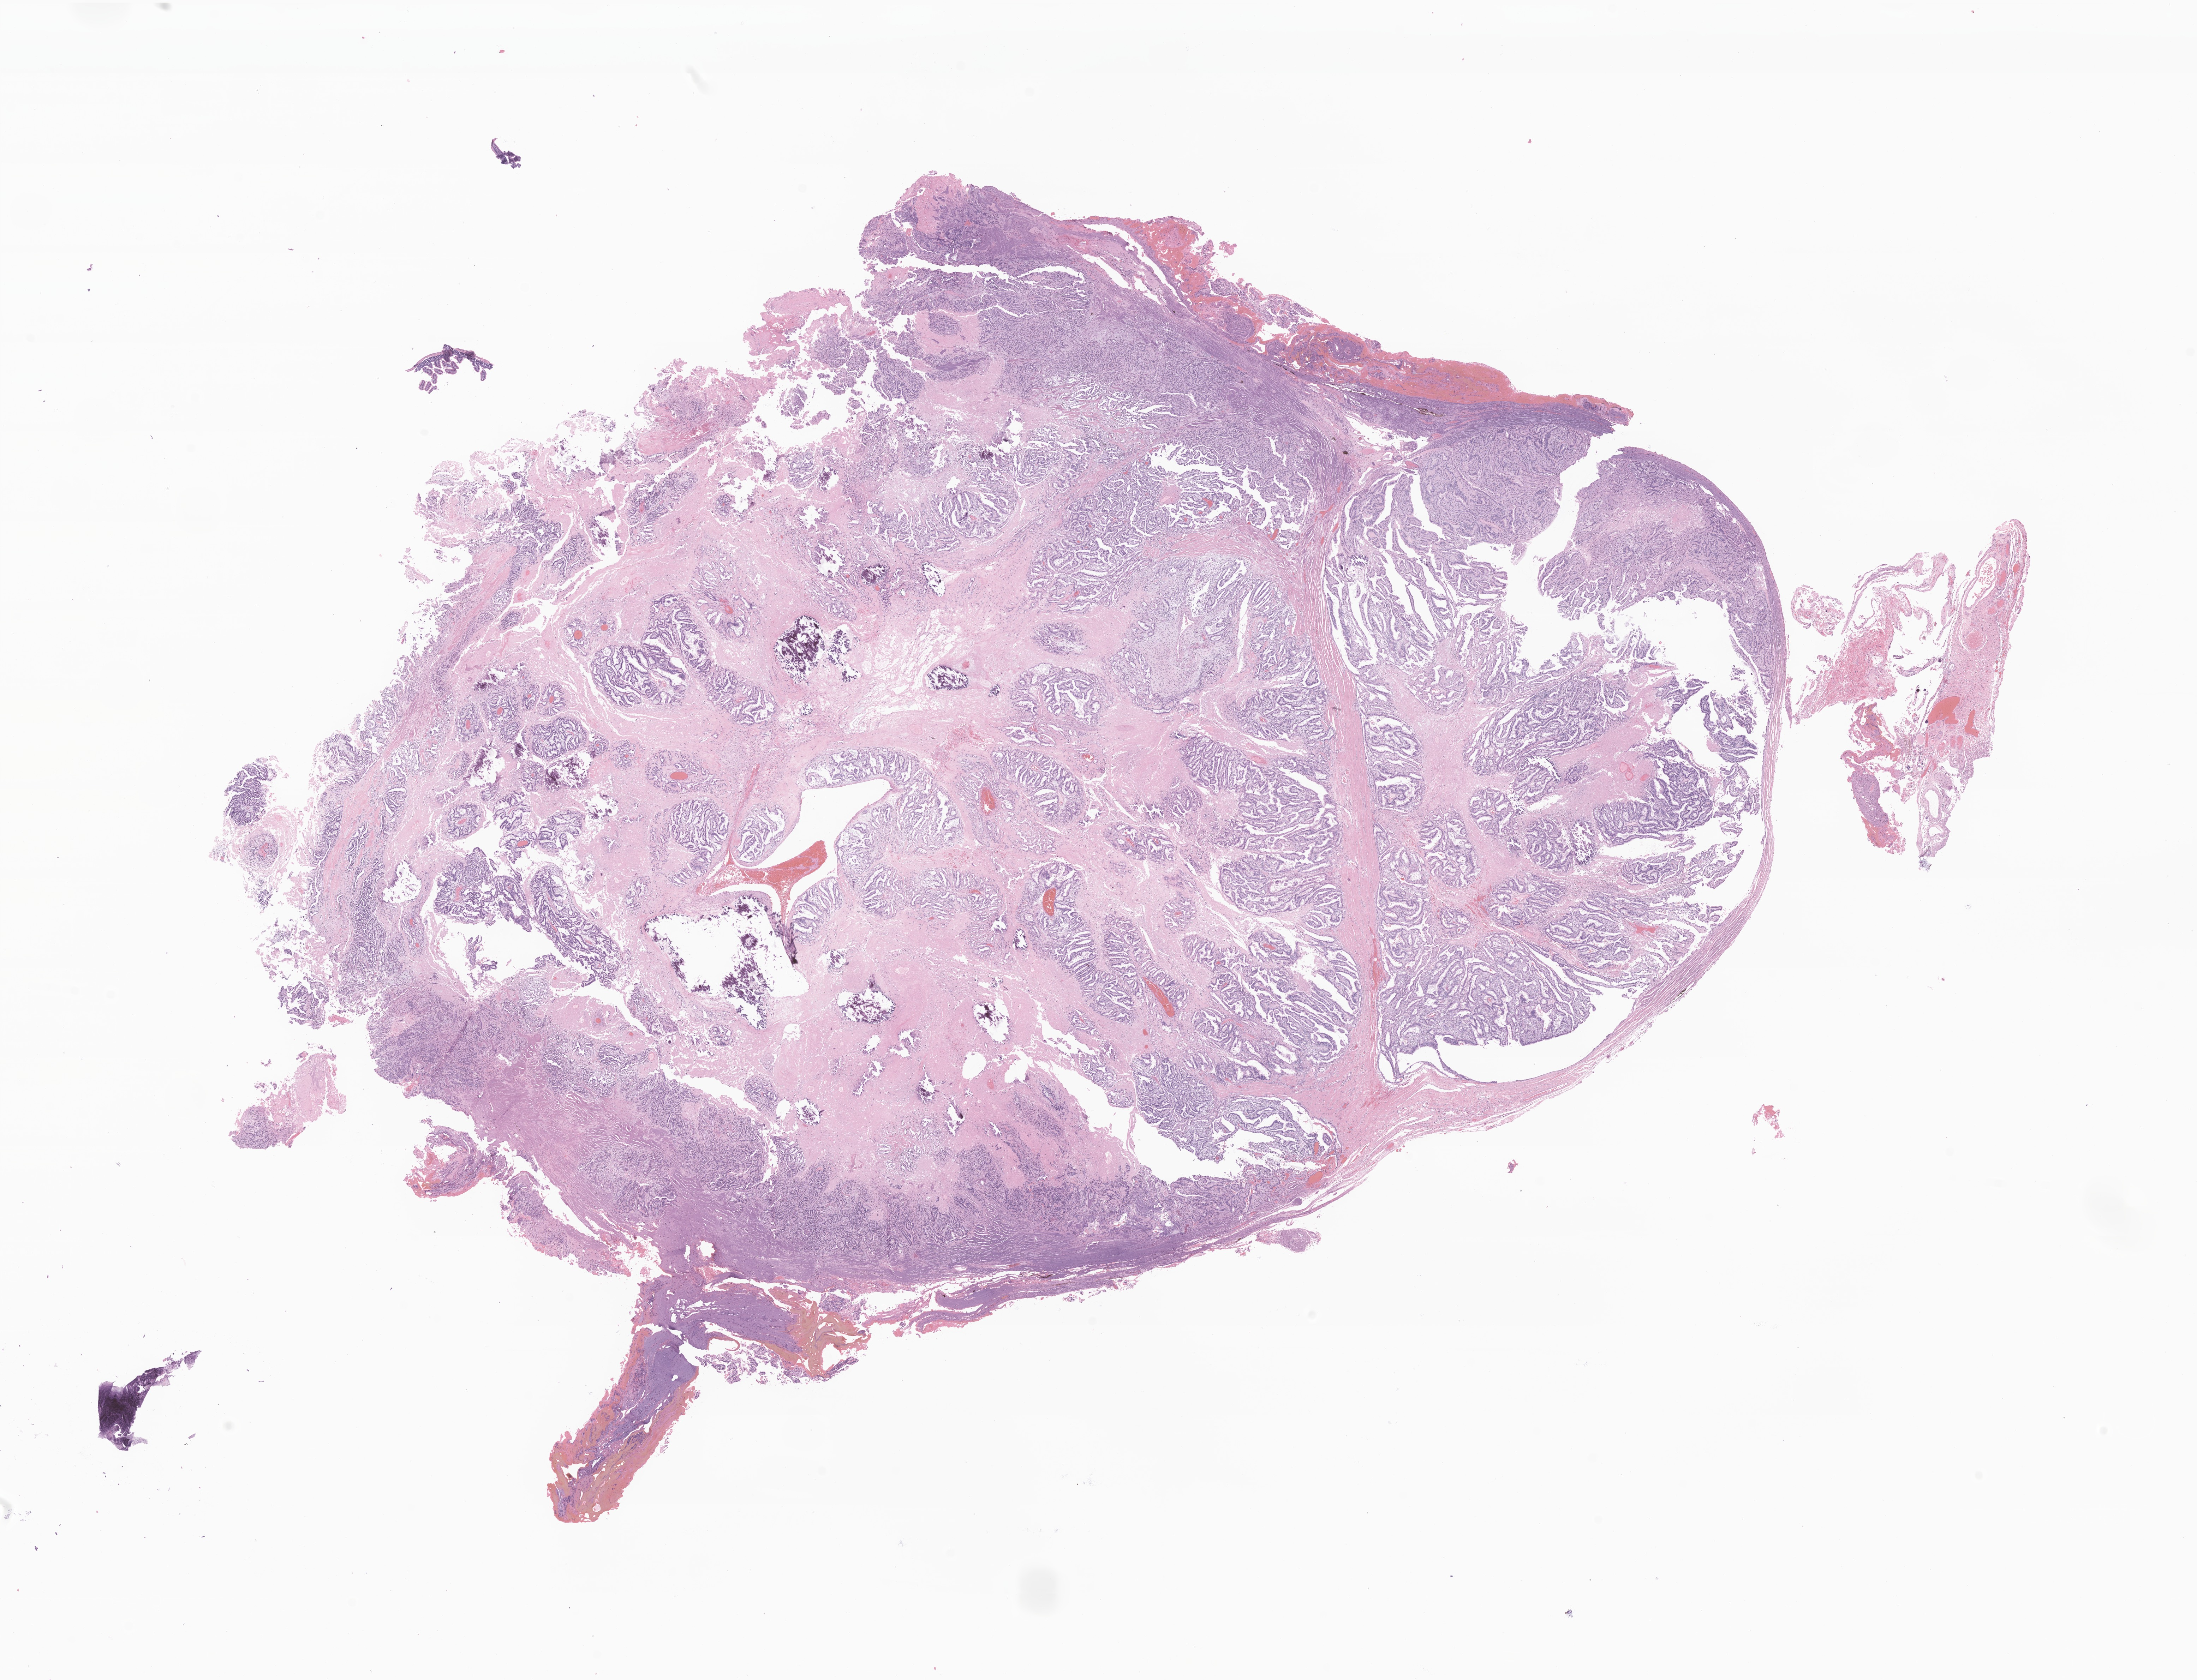
Whole-slide image, haematoxylin and eosin stain of tumor tissue from the brain, whole scanned area (about 26.2 x 20.1 mm) shown as a low-resolution overview. Formalin-fixed paraffin-embedded section. Patient male; age 110 months (9 years 2 months).
Recorded diagnosis: Neoplasm, uncertain whether benign or malignant.